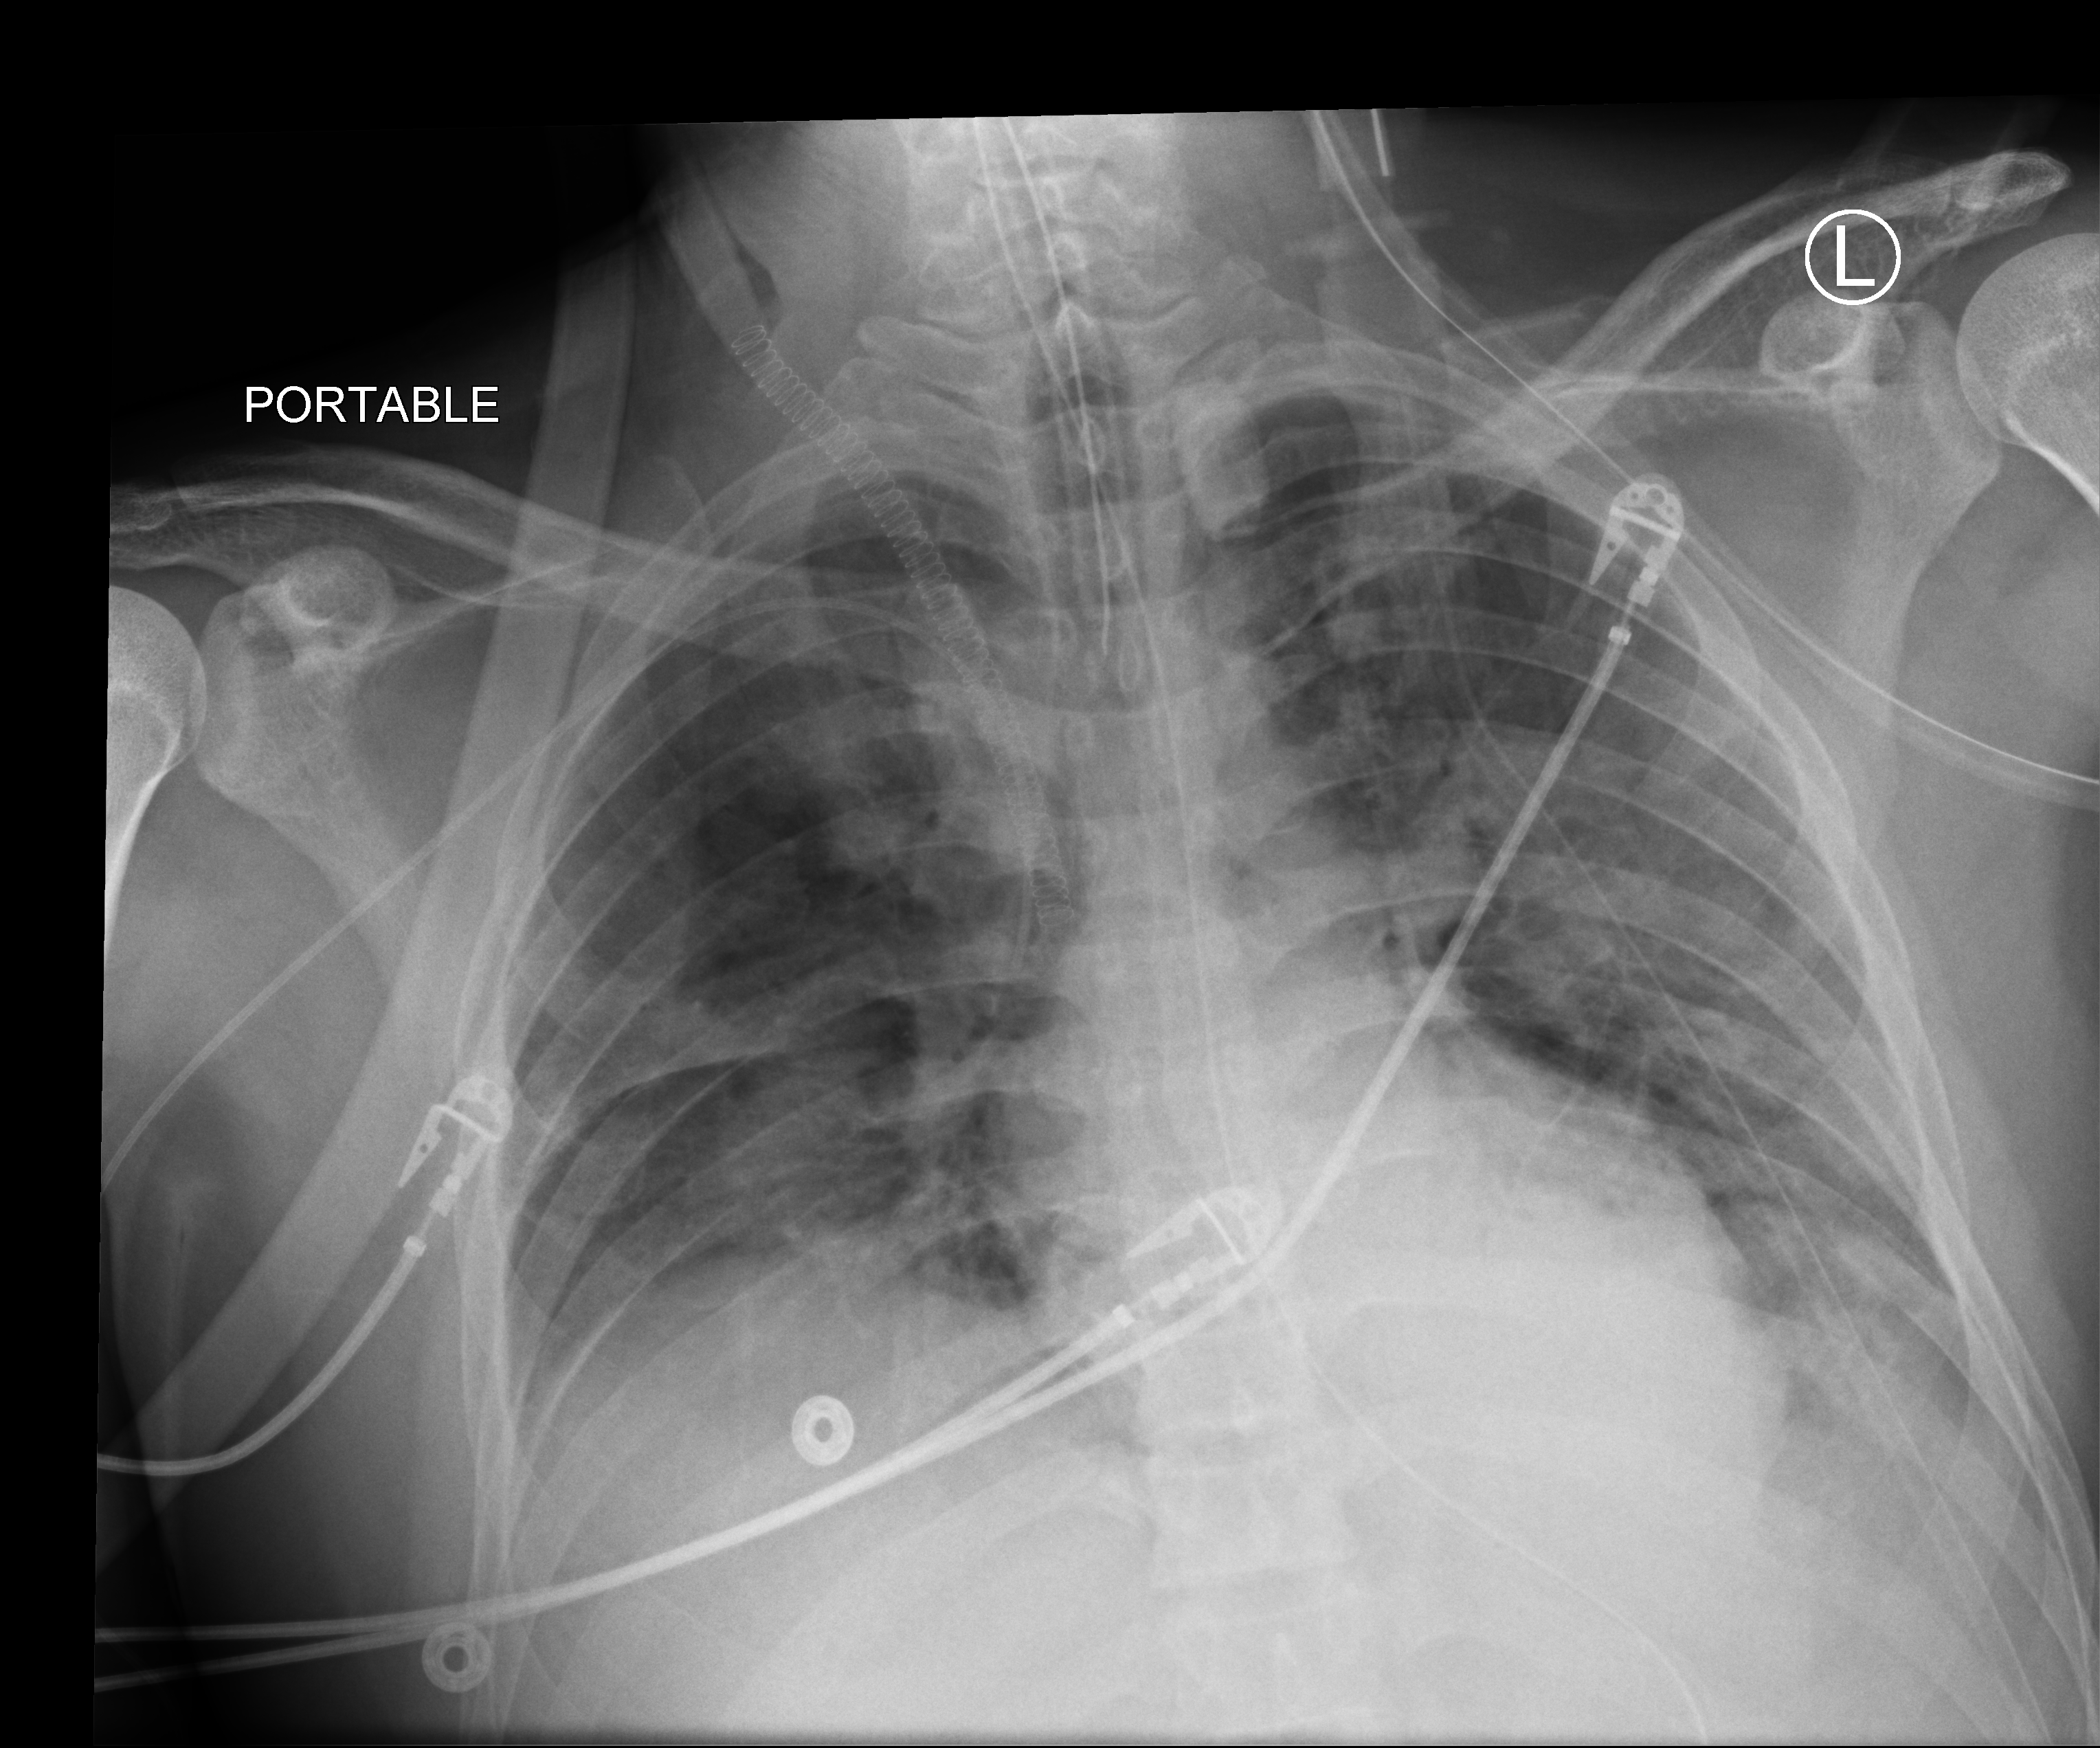
Chest X-ray (portable). Patient hospitalised with COVID-19, aged 18–59 years.
Admission-level facts for this patient (not findings on this image; timing relative to this image not recorded): admitted to intensive care during this hospital stay: yes.